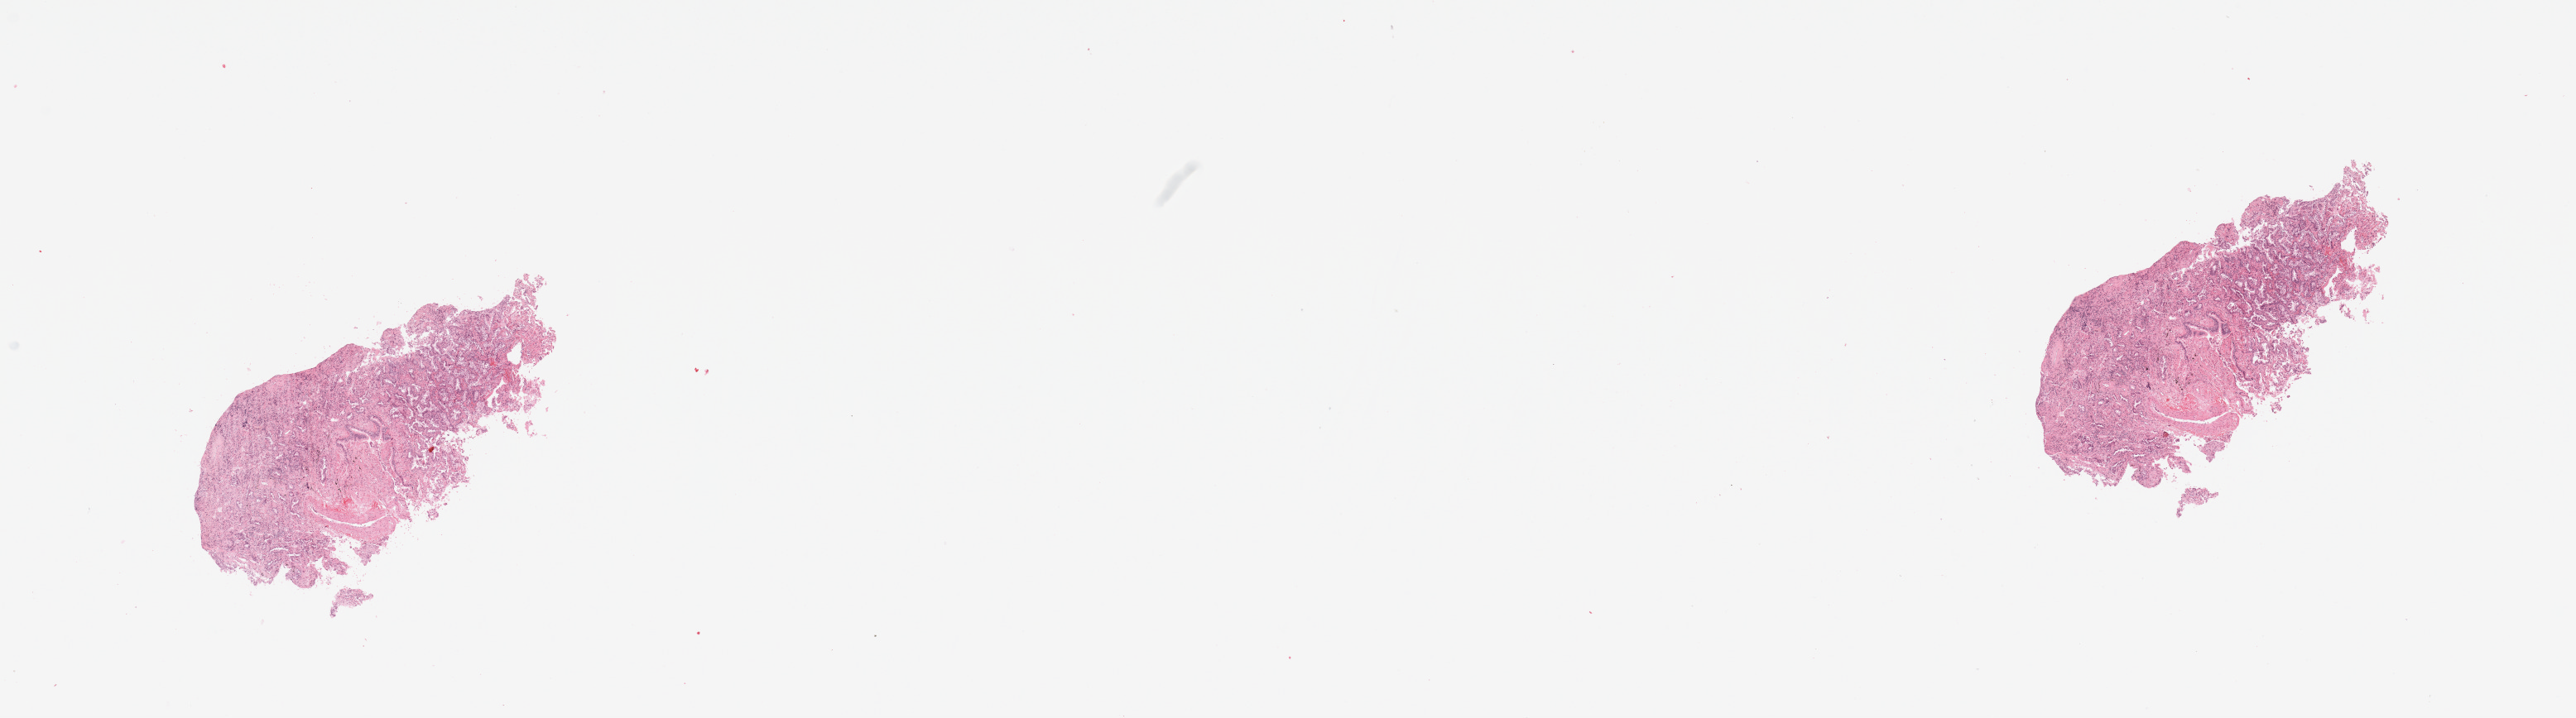
Whole-slide histology image, H&E — a low-resolution overview of the entire scanned area, about 24.6 x 6.9 mm (slide scanned at 20x), lung, tumour tissue. Patient: female, age 78 years. Histologic grade: G2 (moderately differentiated).
- histologic diagnosis: Adenocarcinoma, NOS
- AJCC pathologic stage: IIB